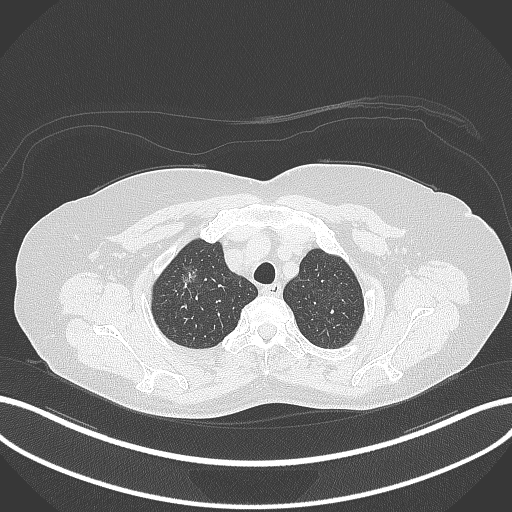
Chest CT, one axial slice; slice 298 of 365 in the series (ordered by position); lung window (W 1500 / L -600 HU); 1 mm slice thickness; 512 × 512 image matrix, field of view 400 × 400 mm. Female patient, age 62 years. Case-level facts recorded for this patient, not image findings: clinical TNM (as recorded): T1c N0 M0.
Outlined on this slice (rectangle marked by the reading radiologist):
- lung tumour (recorded histology: adenocarcinoma): bounding box [x1, y1, x2, y2] px = [176, 250, 205, 291]